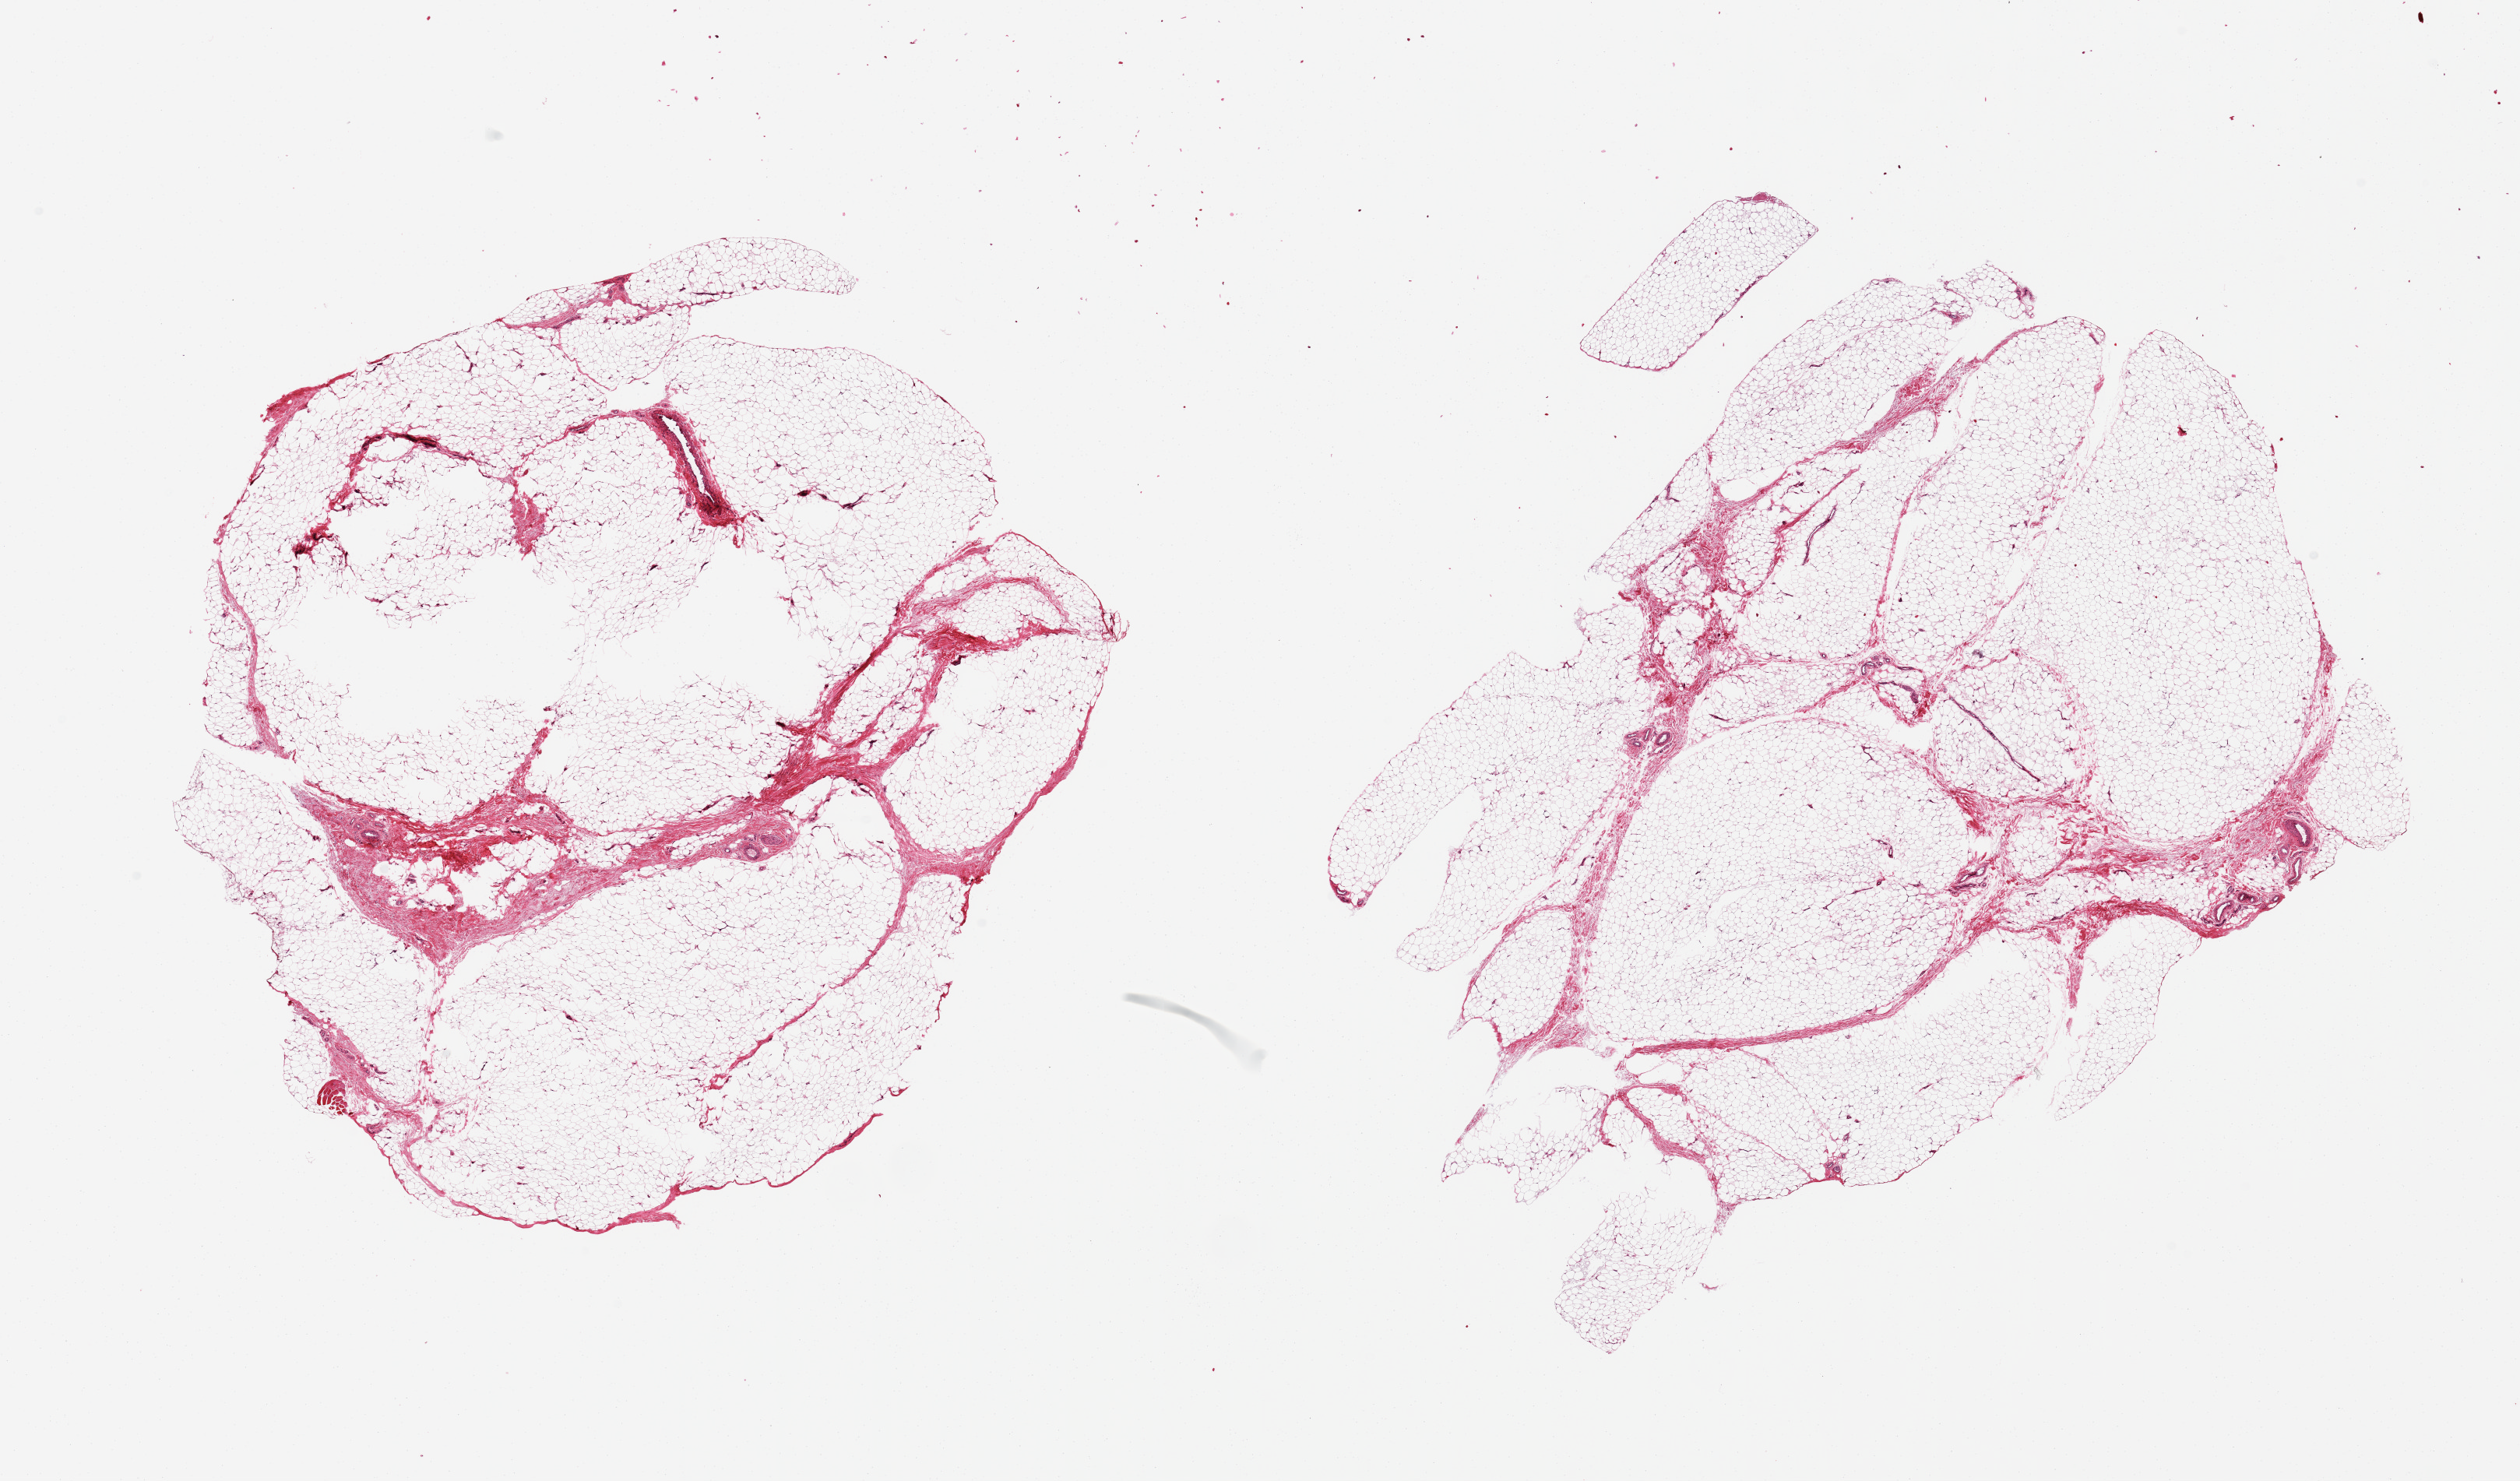
H&E whole-slide image — whole scanned area (about 25.6 x 15.0 mm, acquisition: 20x scan) shown as a low-resolution overview. PAXgene-fixed, paraffin-embedded tissue. Sampled site (target tissue): adipose tissue. Donor tissue sample. Donor sex: male.
Reviewer comment on this tissue sample: 2 pieces; 5% fibrous content; central holes in 1 piece.